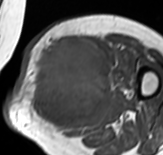
MRI of an extremity soft-tissue mass, one axial slice. Position 38 of 65 along the scan axis. MR volume resampled by the dataset authors to the PET/CT grid (not the native acquisition matrix). 163 × 155 image matrix, field of view 159 × 151 mm. Female patient. Case-level facts recorded for this patient, not image findings: histological type: pleomorphic leiomyosarcoma; grade: high; site of the primary tumour: left thigh.
Structures marked on this image (expert contour drawn on MRI and transferred to this co-registered scan by the dataset authors):
- gross tumour volume including surrounding oedema: bounding box <32,37,113,134> (left, top, right, bottom; pixels)
- gross tumour volume (mass): <33,37,109,130>